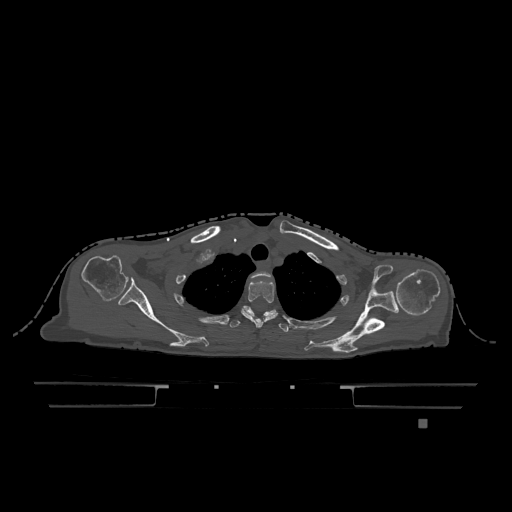
CT including the spine, one axial slice. Slice 954 of 1317 in the series (ordered by position). Bone window (W 1800 / L 400 HU). 0.5 mm slice thickness. 512 × 512 image matrix, field of view 500 × 500 mm. Female patient, age 74 years. From the clinical record (not read from this slice): primary cancer: lung.
Annotated regions visible in this slice (semi-automatic segmentation, software-assisted and operator-edited):
- T1 vertebra: bounding box [x1, y1, x2, y2] px = [252, 272, 271, 278]
- T2 vertebra: [241, 280, 278, 328]
- T3 vertebra: [230, 308, 289, 332]
- T6 vertebra: [242, 306, 276, 317]